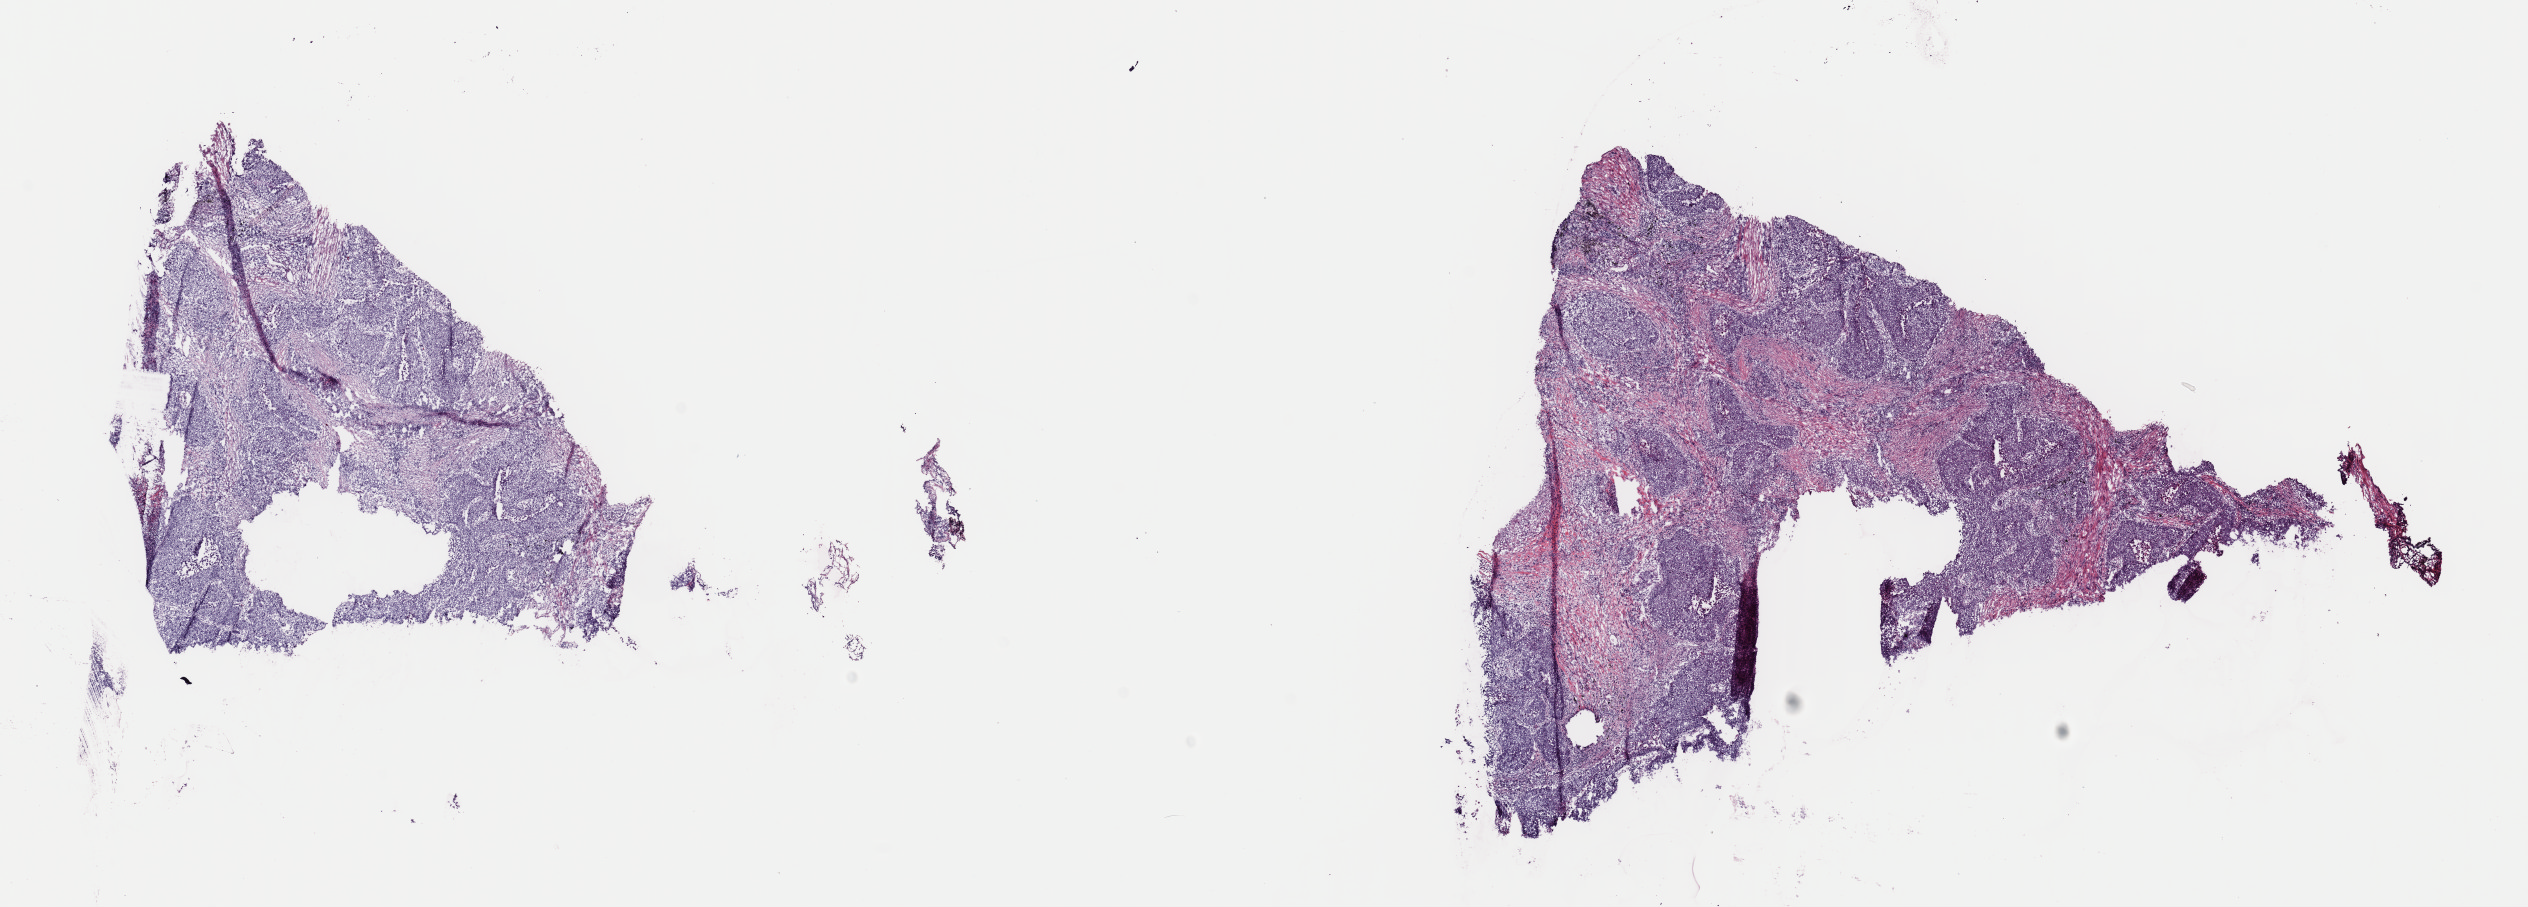
Whole-slide histology image, H&E, a low-resolution overview of the entire scanned area, about 20.0 x 7.2 mm (slide scanned at 40x); frozen section from the top of the tissue portion; sample: primary tumour, lung. Male patient; age at initial diagnosis 65 years. Pathologist review of this section (percent, as recorded): tumour cells 100%, tumour nuclei 80%, normal cells 0%, stromal cells 0%, necrosis 0%. Infiltration values recorded for this section: lymphocyte infiltration 3%, monocyte infiltration 0%, neutrophil infiltration 0%.
AJCC pathologic stage: IIA. Histologic diagnosis: Squamous cell carcinoma, NOS (upper lobe, lung). Laterality: right.